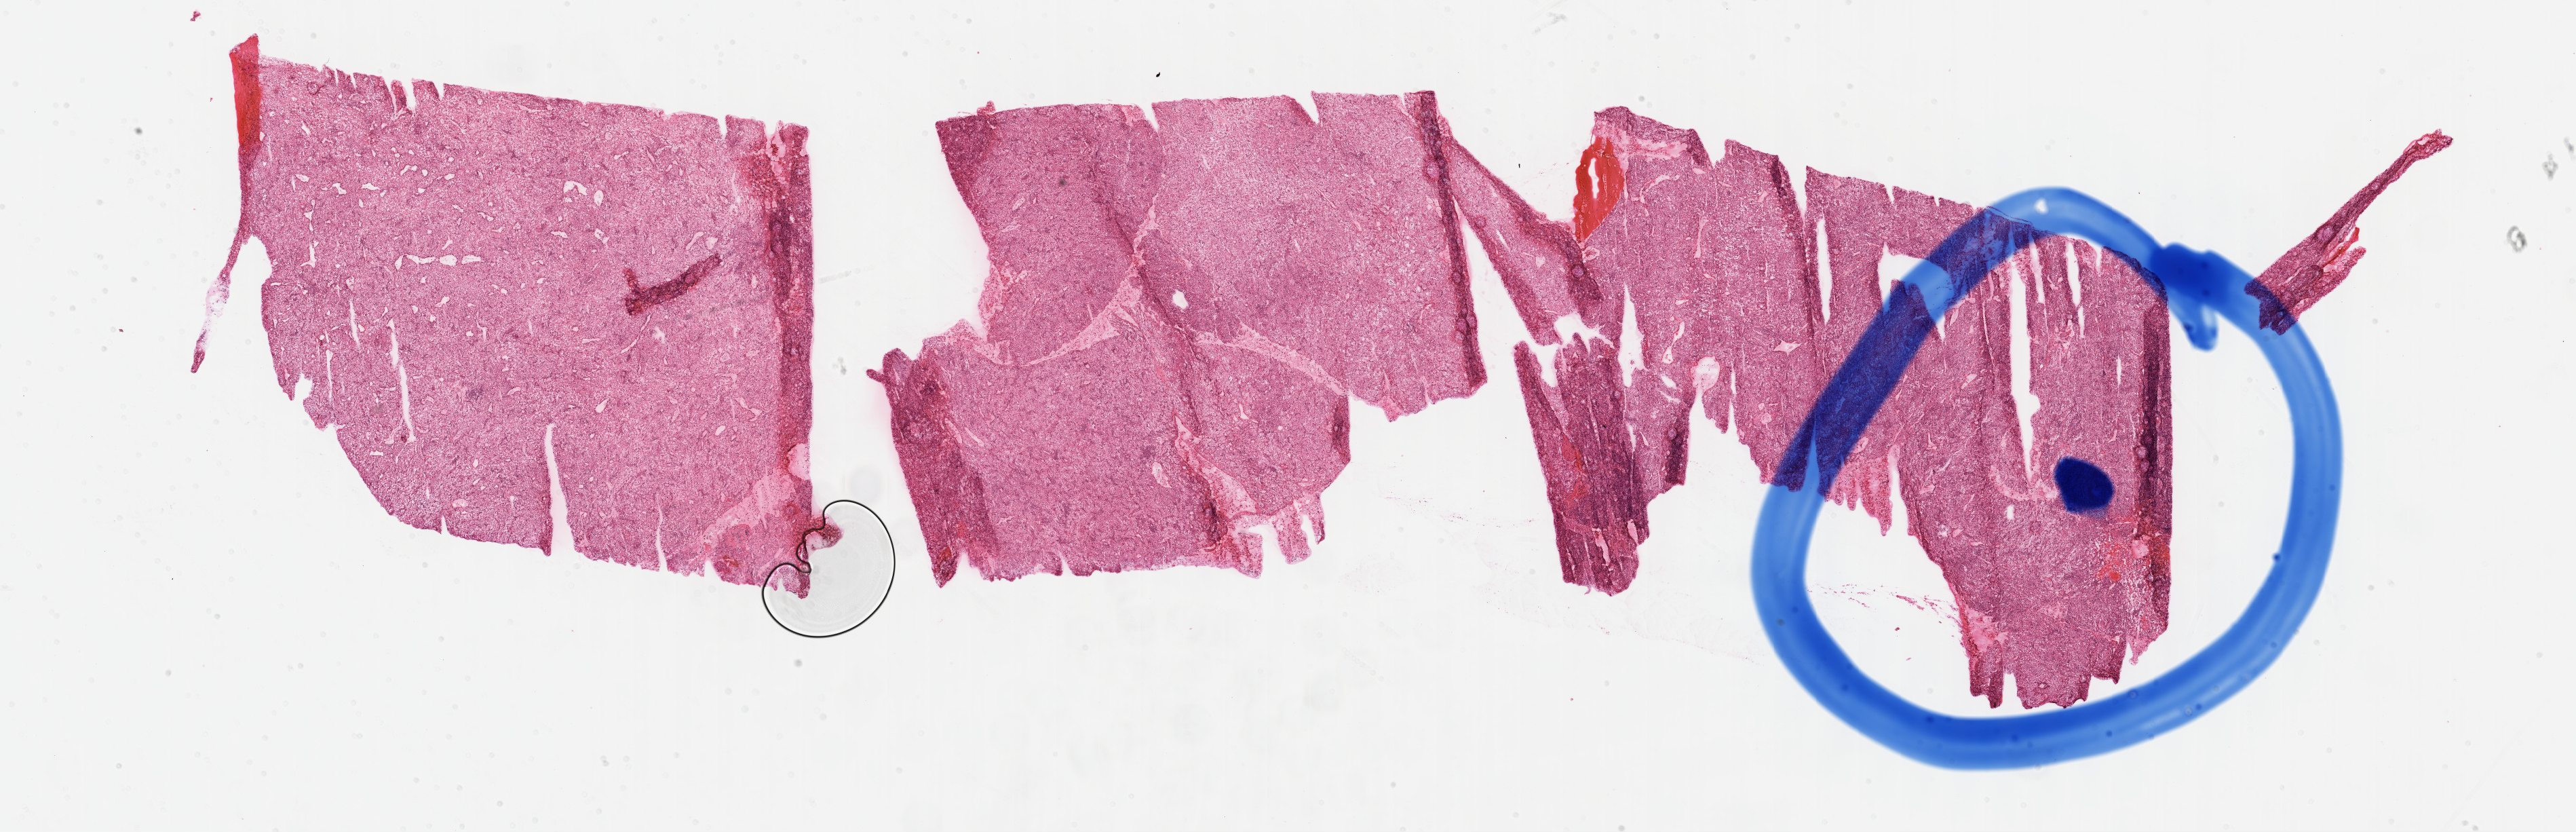
Digitized Hematoxylin and eosin (H&E) stained tissue section (whole slide) — shown as a low-resolution overview of the whole scanned area (about 30.7 x 9.9 mm, acquisition: 40x scan). Formalin-fixed paraffin-embedded (FFPE) diagnostic section. Primary tumour sample from the kidney. Male patient; age at initial diagnosis 62 years. Histologic grade: G3 (poorly differentiated).
Pathologic diagnosis: Clear cell adenocarcinoma, NOS. AJCC pathologic stage: IV.